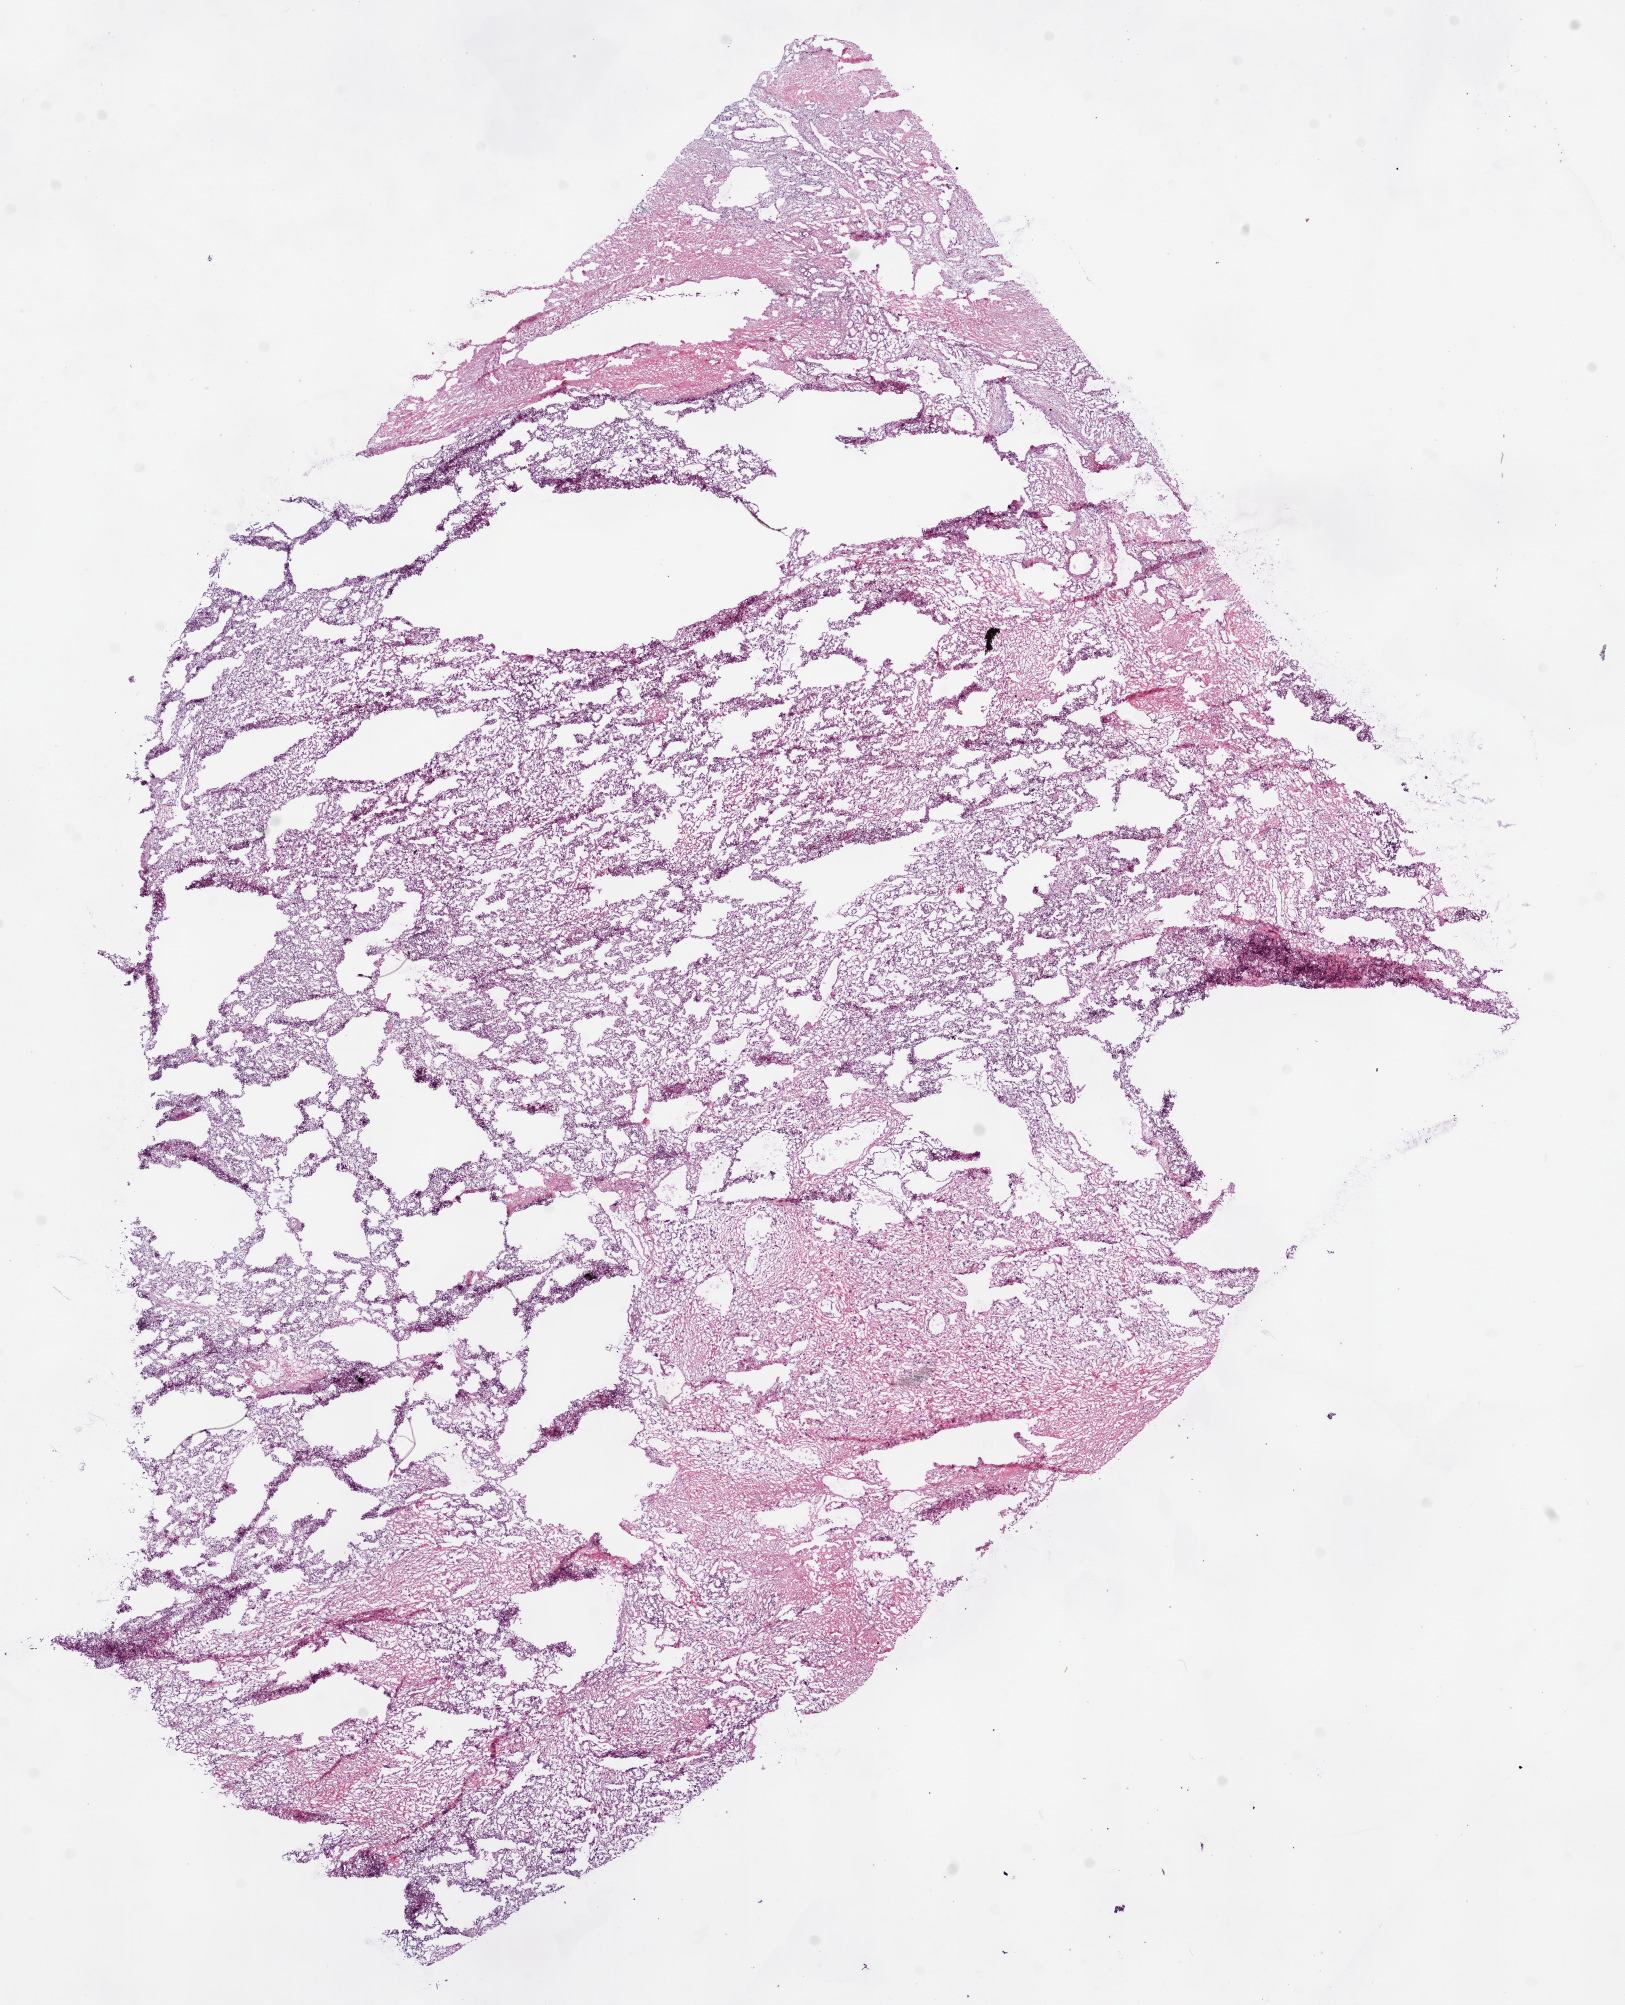
Digitized H&E tissue section (whole slide) — low-resolution overview of the scanned area, about 13.0 x 16.1 mm (acquisition: 20x scan), frozen section, primary tumour sample from the kidney. Male patient; age at initial diagnosis 47 years. Histologic grade: G3 (poorly differentiated). Composition of this section per pathologist review: tumour cells 85%, tumour nuclei 80%, normal cells 0%, stromal cells 15%, necrosis 0%.
* AJCC pathologic stage: III
* laterality: left
* diagnosis: Clear cell adenocarcinoma, NOS
* lymph nodes positive (case pathology): 2 of 6 examined